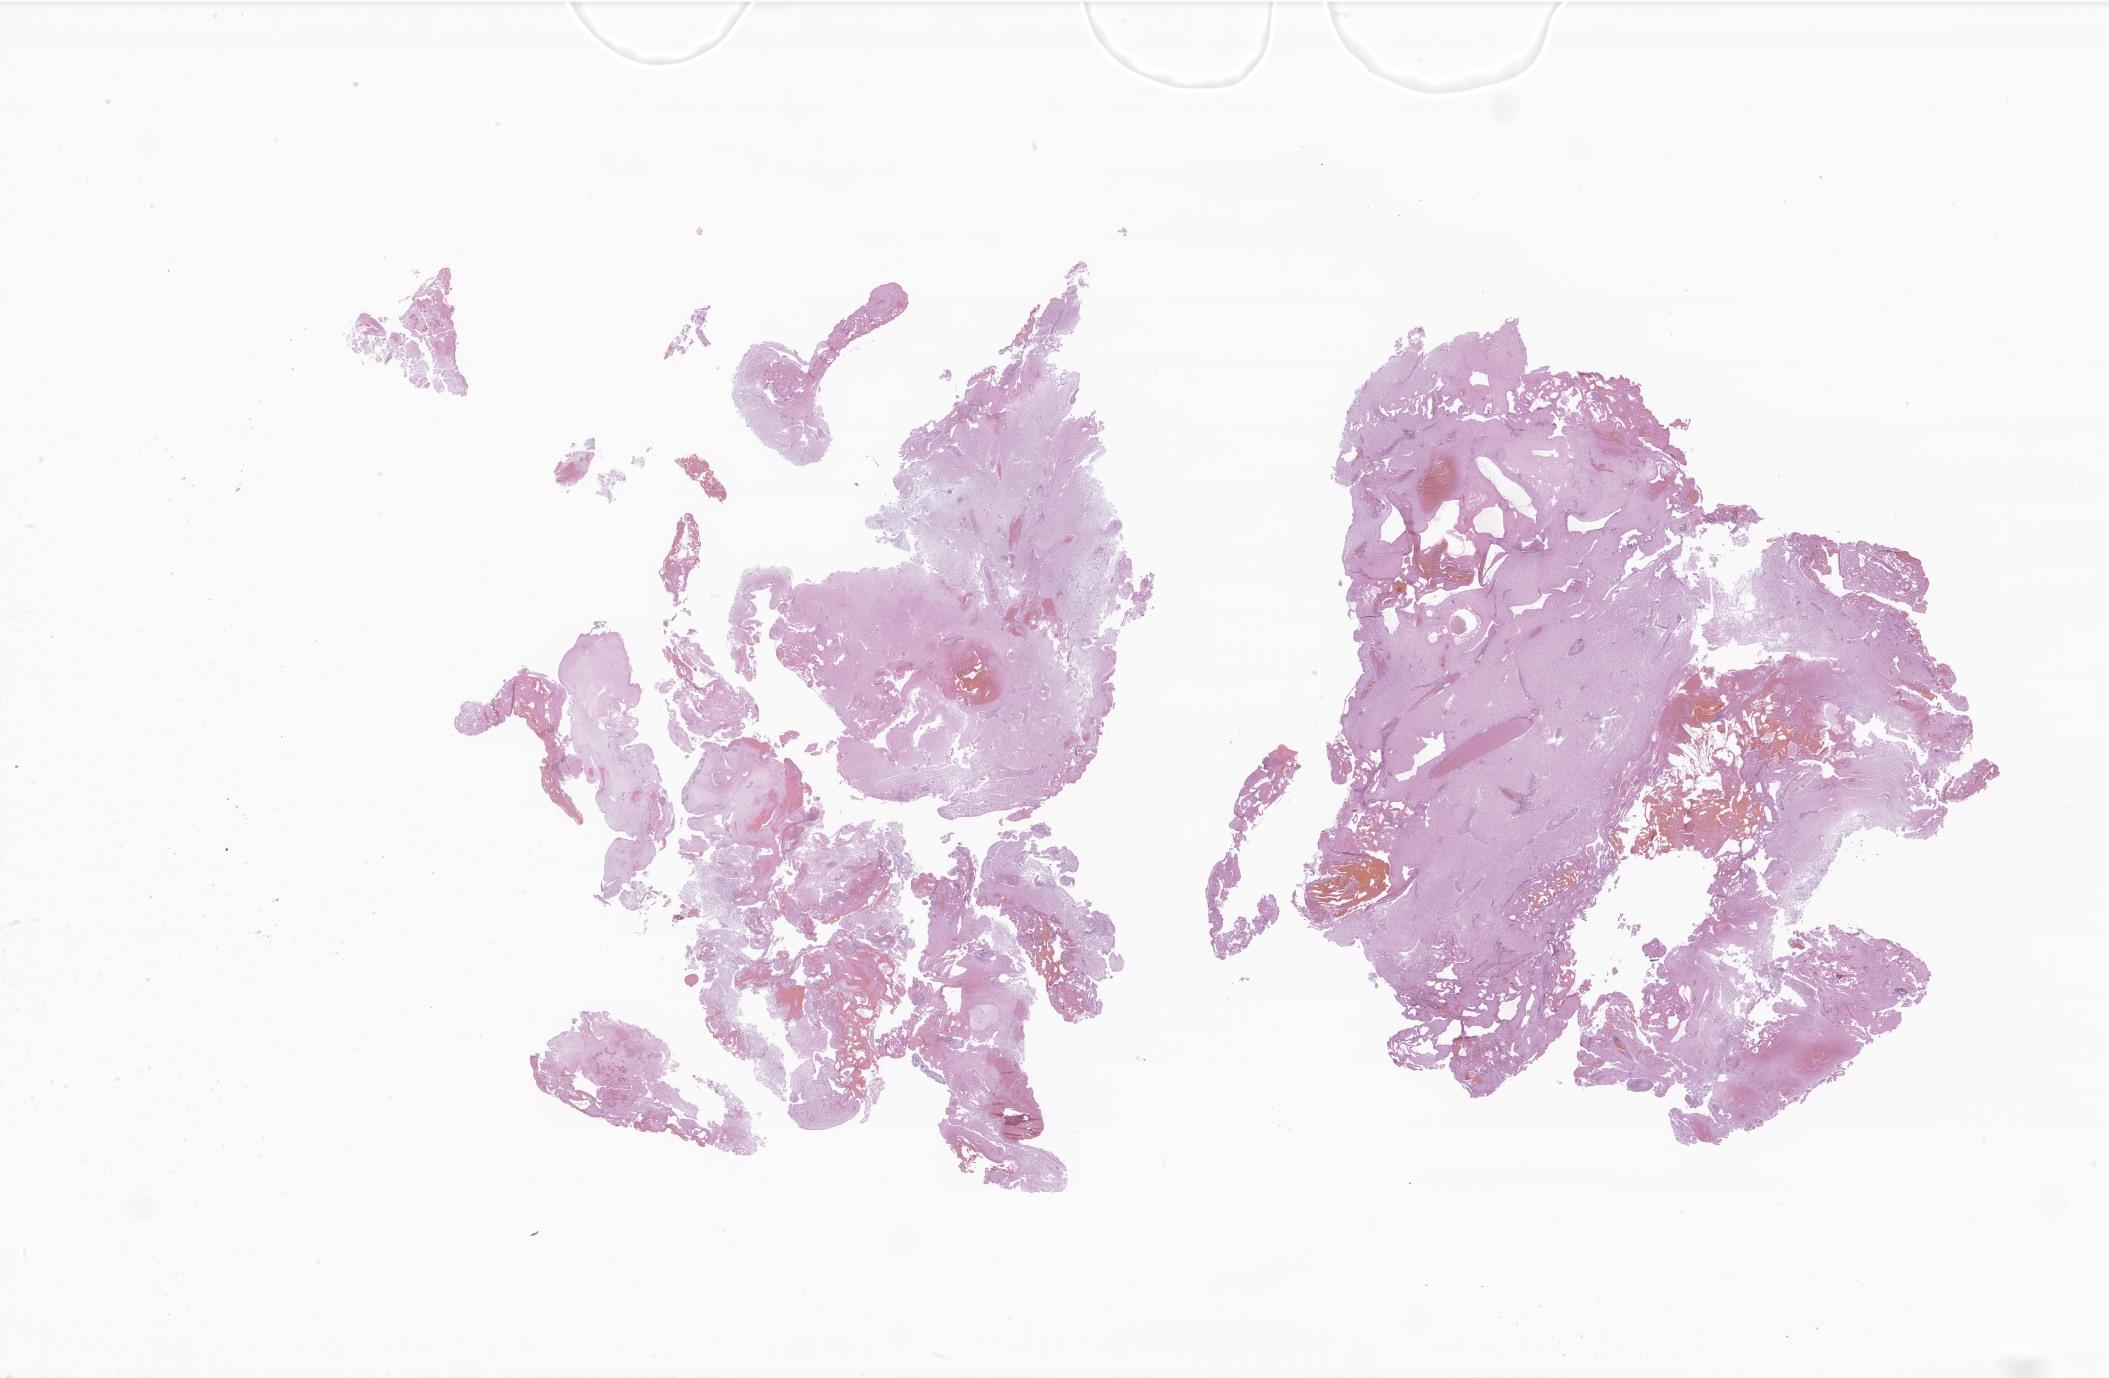
Hematoxylin and eosin (H&E) whole-slide image of tumor tissue from the brain — shown as a low-resolution overview of the whole scanned area (about 35.6 x 23.2 mm). FFPE section. Female patient, age 126 months.
Diagnosis (ICD-O-3 morphology term): Pilocytic astrocytoma.